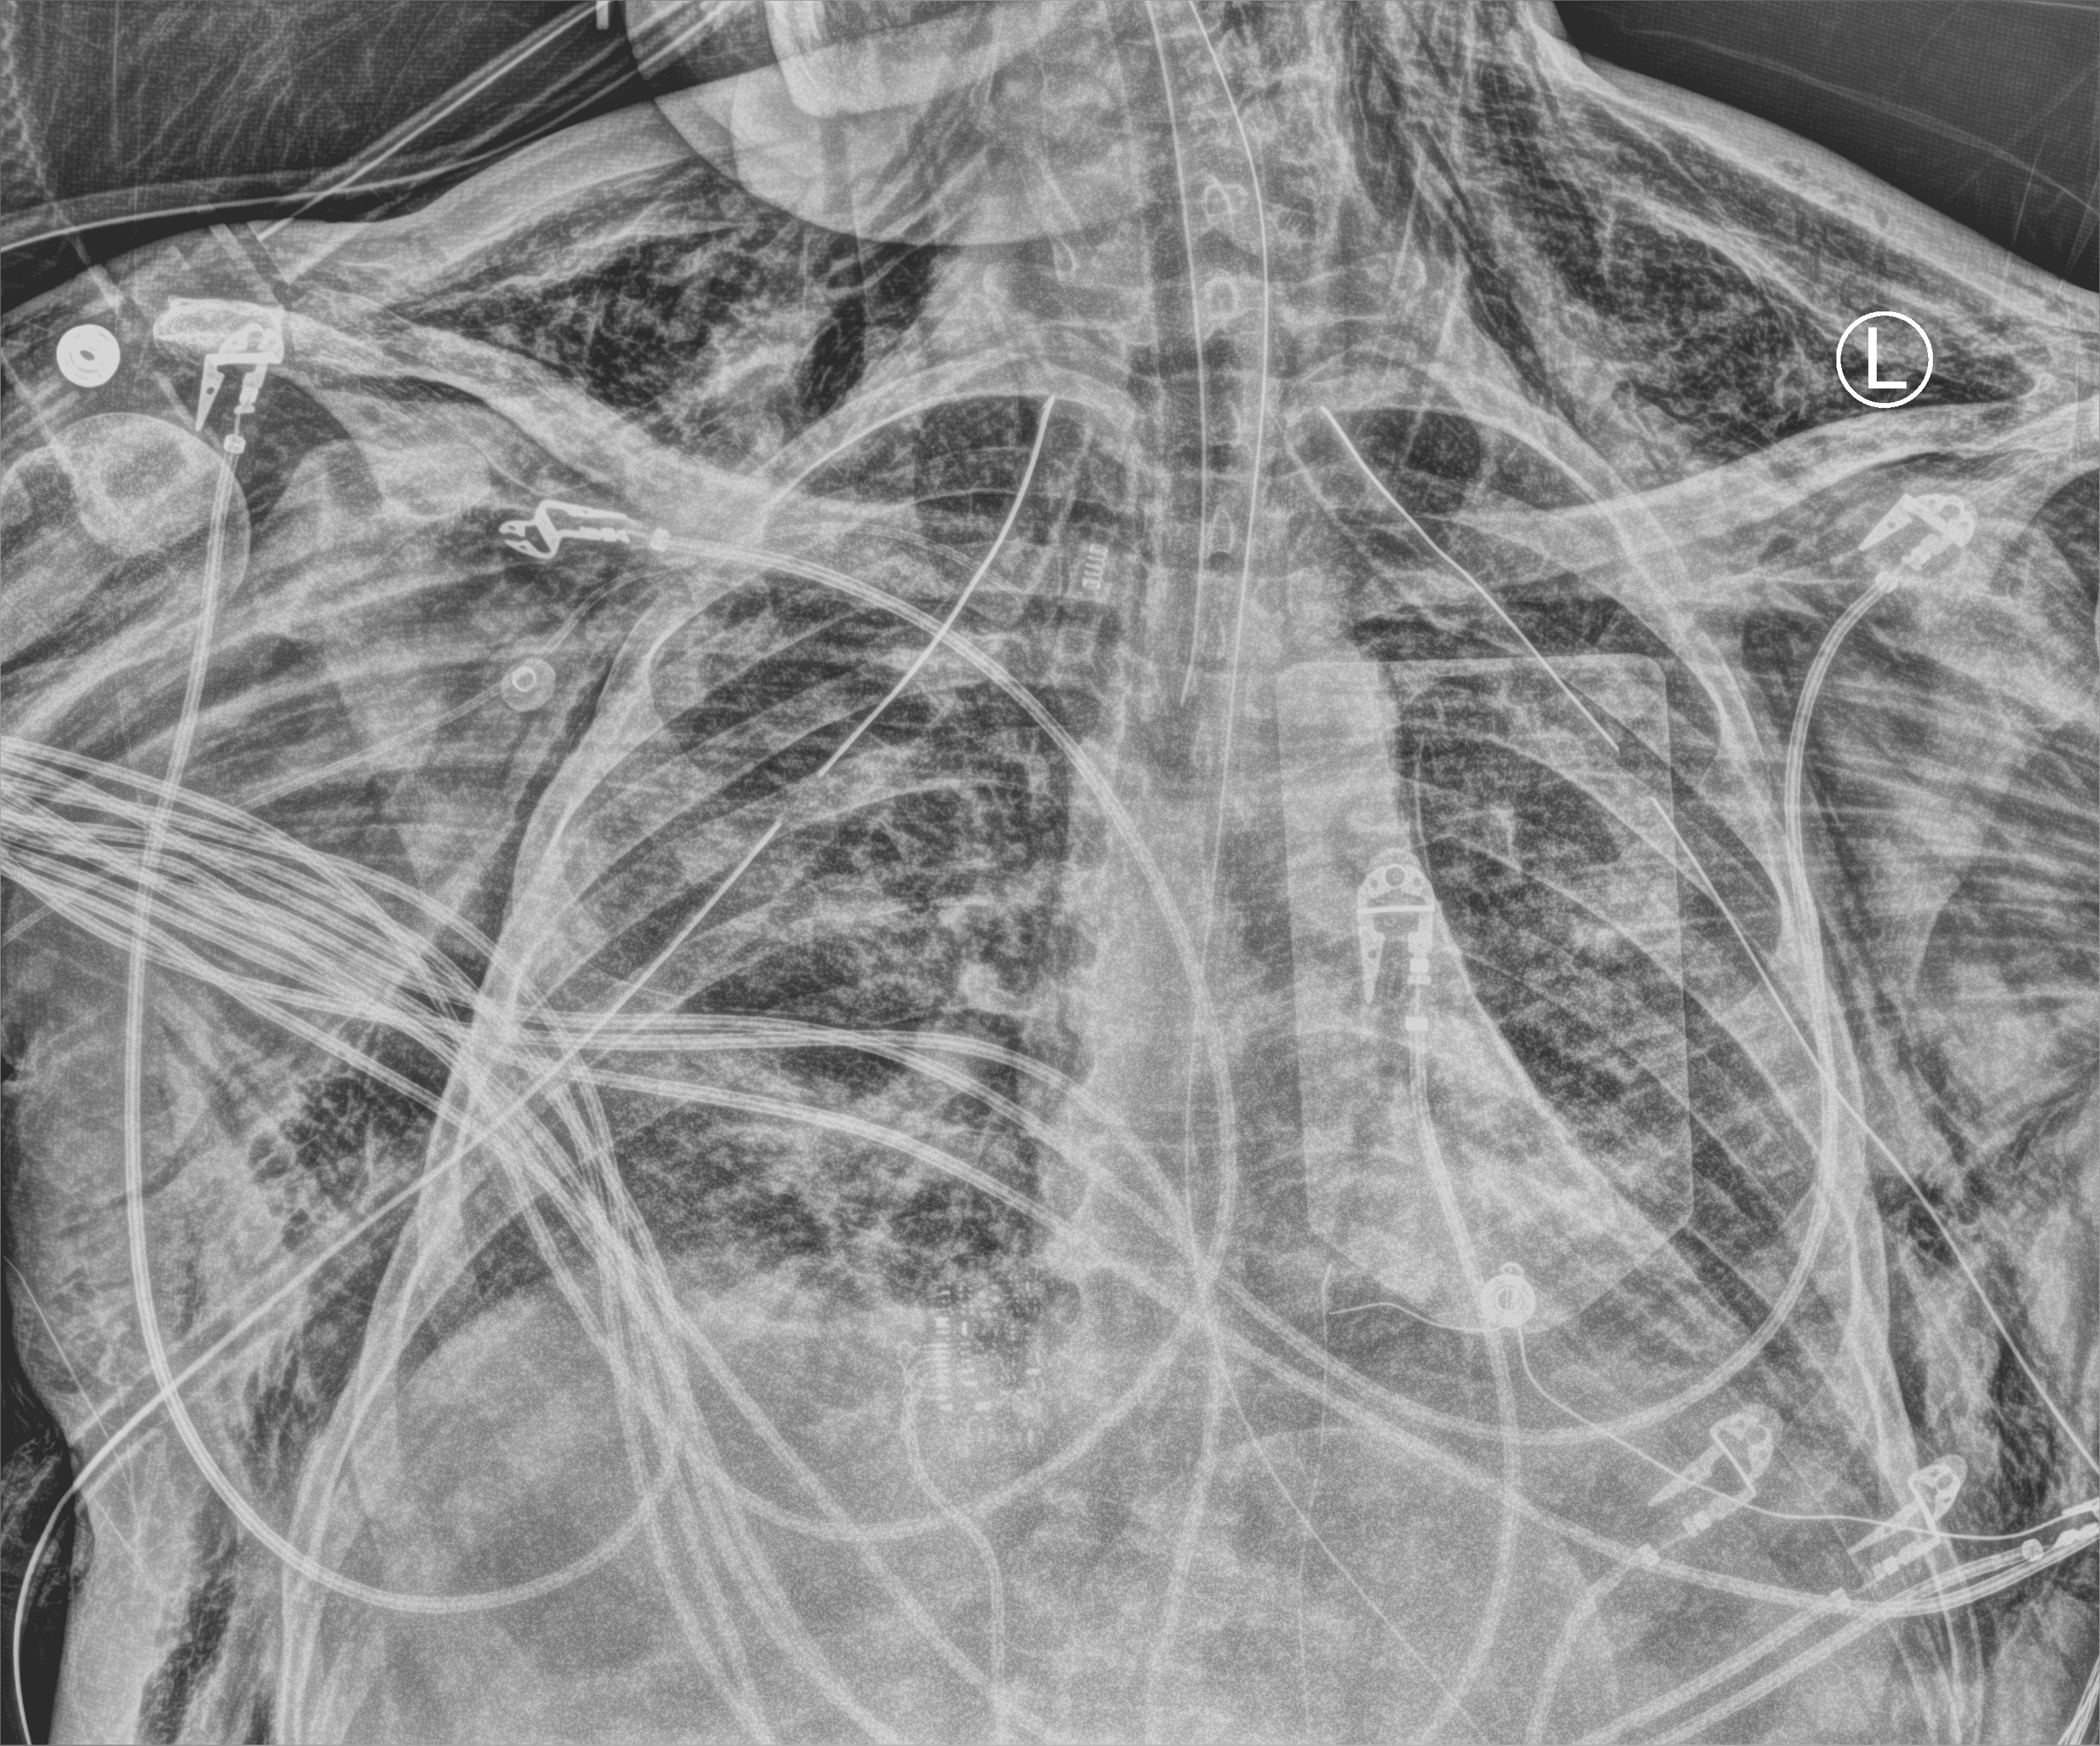
Bedside chest radiograph (computed radiography); anteroposterior (AP) projection. Patient hospitalised with COVID-19; male, aged 18–59 years.
Hospital-stay facts (about this admission, not read from this image; timing relative to this image not recorded):
- length of hospital stay: 83 days
- admitted to intensive care during this hospital stay: yes